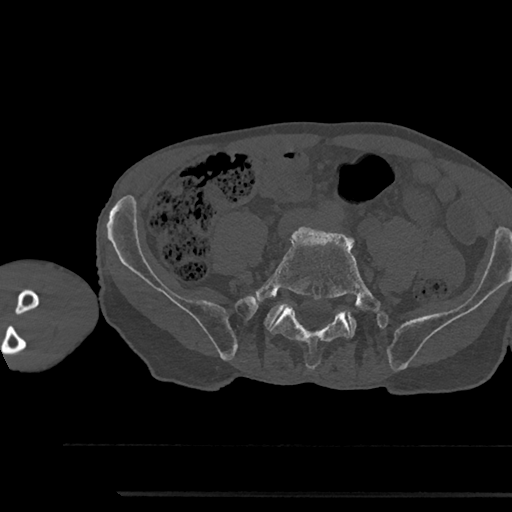
CT including the spine, one axial slice; reconstruction kernel Br40s/3; 120 kVp; bone window (W 1800 / L 400 HU); 0.5 mm slice thickness; 512 × 512 image matrix, field of view 367 × 367 mm. Male patient, age 79 years. From the clinical record (not read from this slice): primary cancer: prostate.
Annotated regions visible in this slice (semi-automatic segmentation, software-assisted and operator-edited):
- L5 vertebra: bounding box <253,226,381,370> (left, top, right, bottom; pixels)